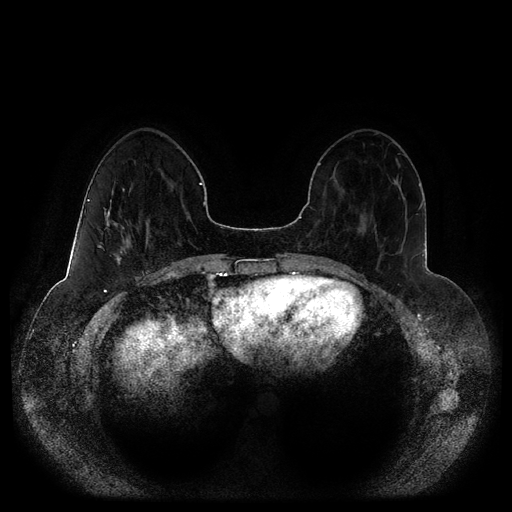
Breast MRI (dynamic contrast-enhanced, multi-phase), one axial slice. Position 34 of 116 along the scan axis. Dynamic contrast-enhanced series, time point 2 of 5 at this slice position (early post-contrast). 1.5 T. TE 2.5 ms, TR 5.2 ms. 2 mm slice thickness. 512 × 512 image matrix, field of view 390 × 390 mm. Patient: female, 44 years.
Annotated regions visible in this slice (semi-automatic segmentation, software-assisted and operator-edited):
- breast lesion (labelled 'tumour' in the annotation; benign lesions carry a separate 'benign' label): bounding box <97,200,137,271> (left, top, right, bottom; pixels)